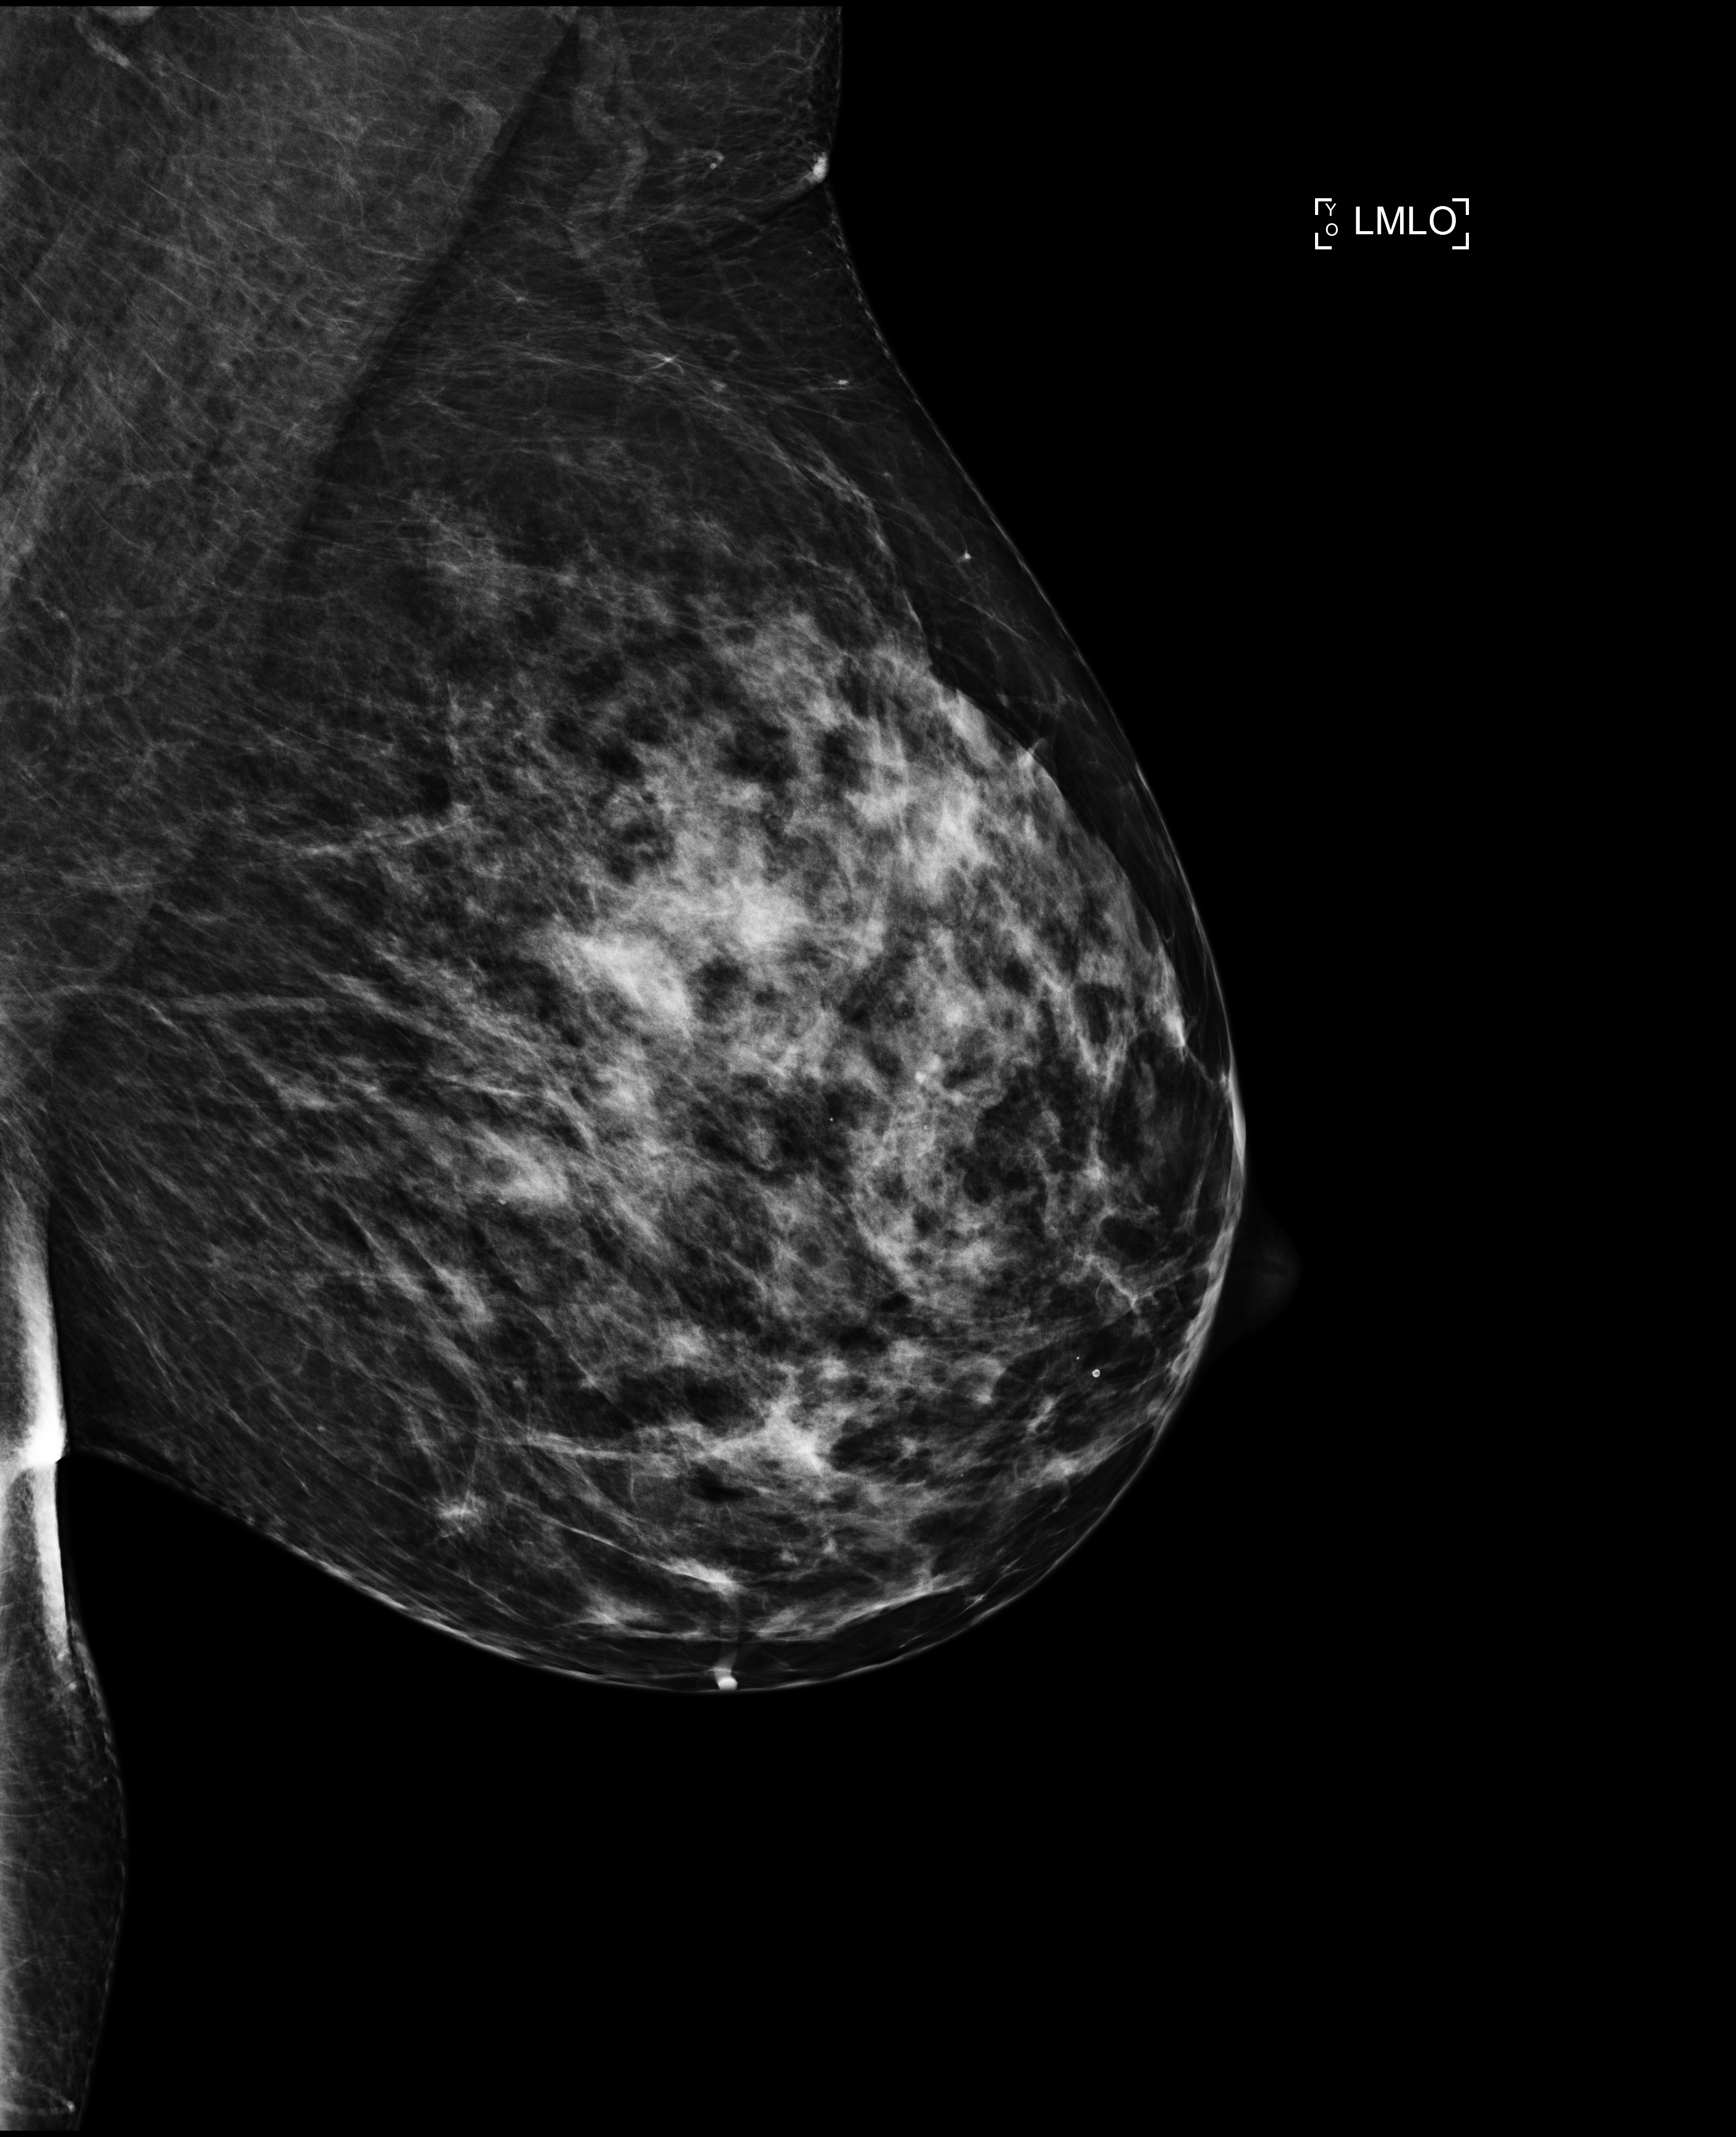
Annual screening mammography examination; system: Selenia Dimensions. Patient aged 45 years (female).
Image type: full-field digital mammogram. Breast: left. Projection: medio-lateral oblique projection. BI-RADS breast density category at the screening exam (both breasts, scale 1–4): 3. Final BI-RADS category for the screening round (tomosynthesis exam, both breasts): category 2. Recall: no recall after this screen.